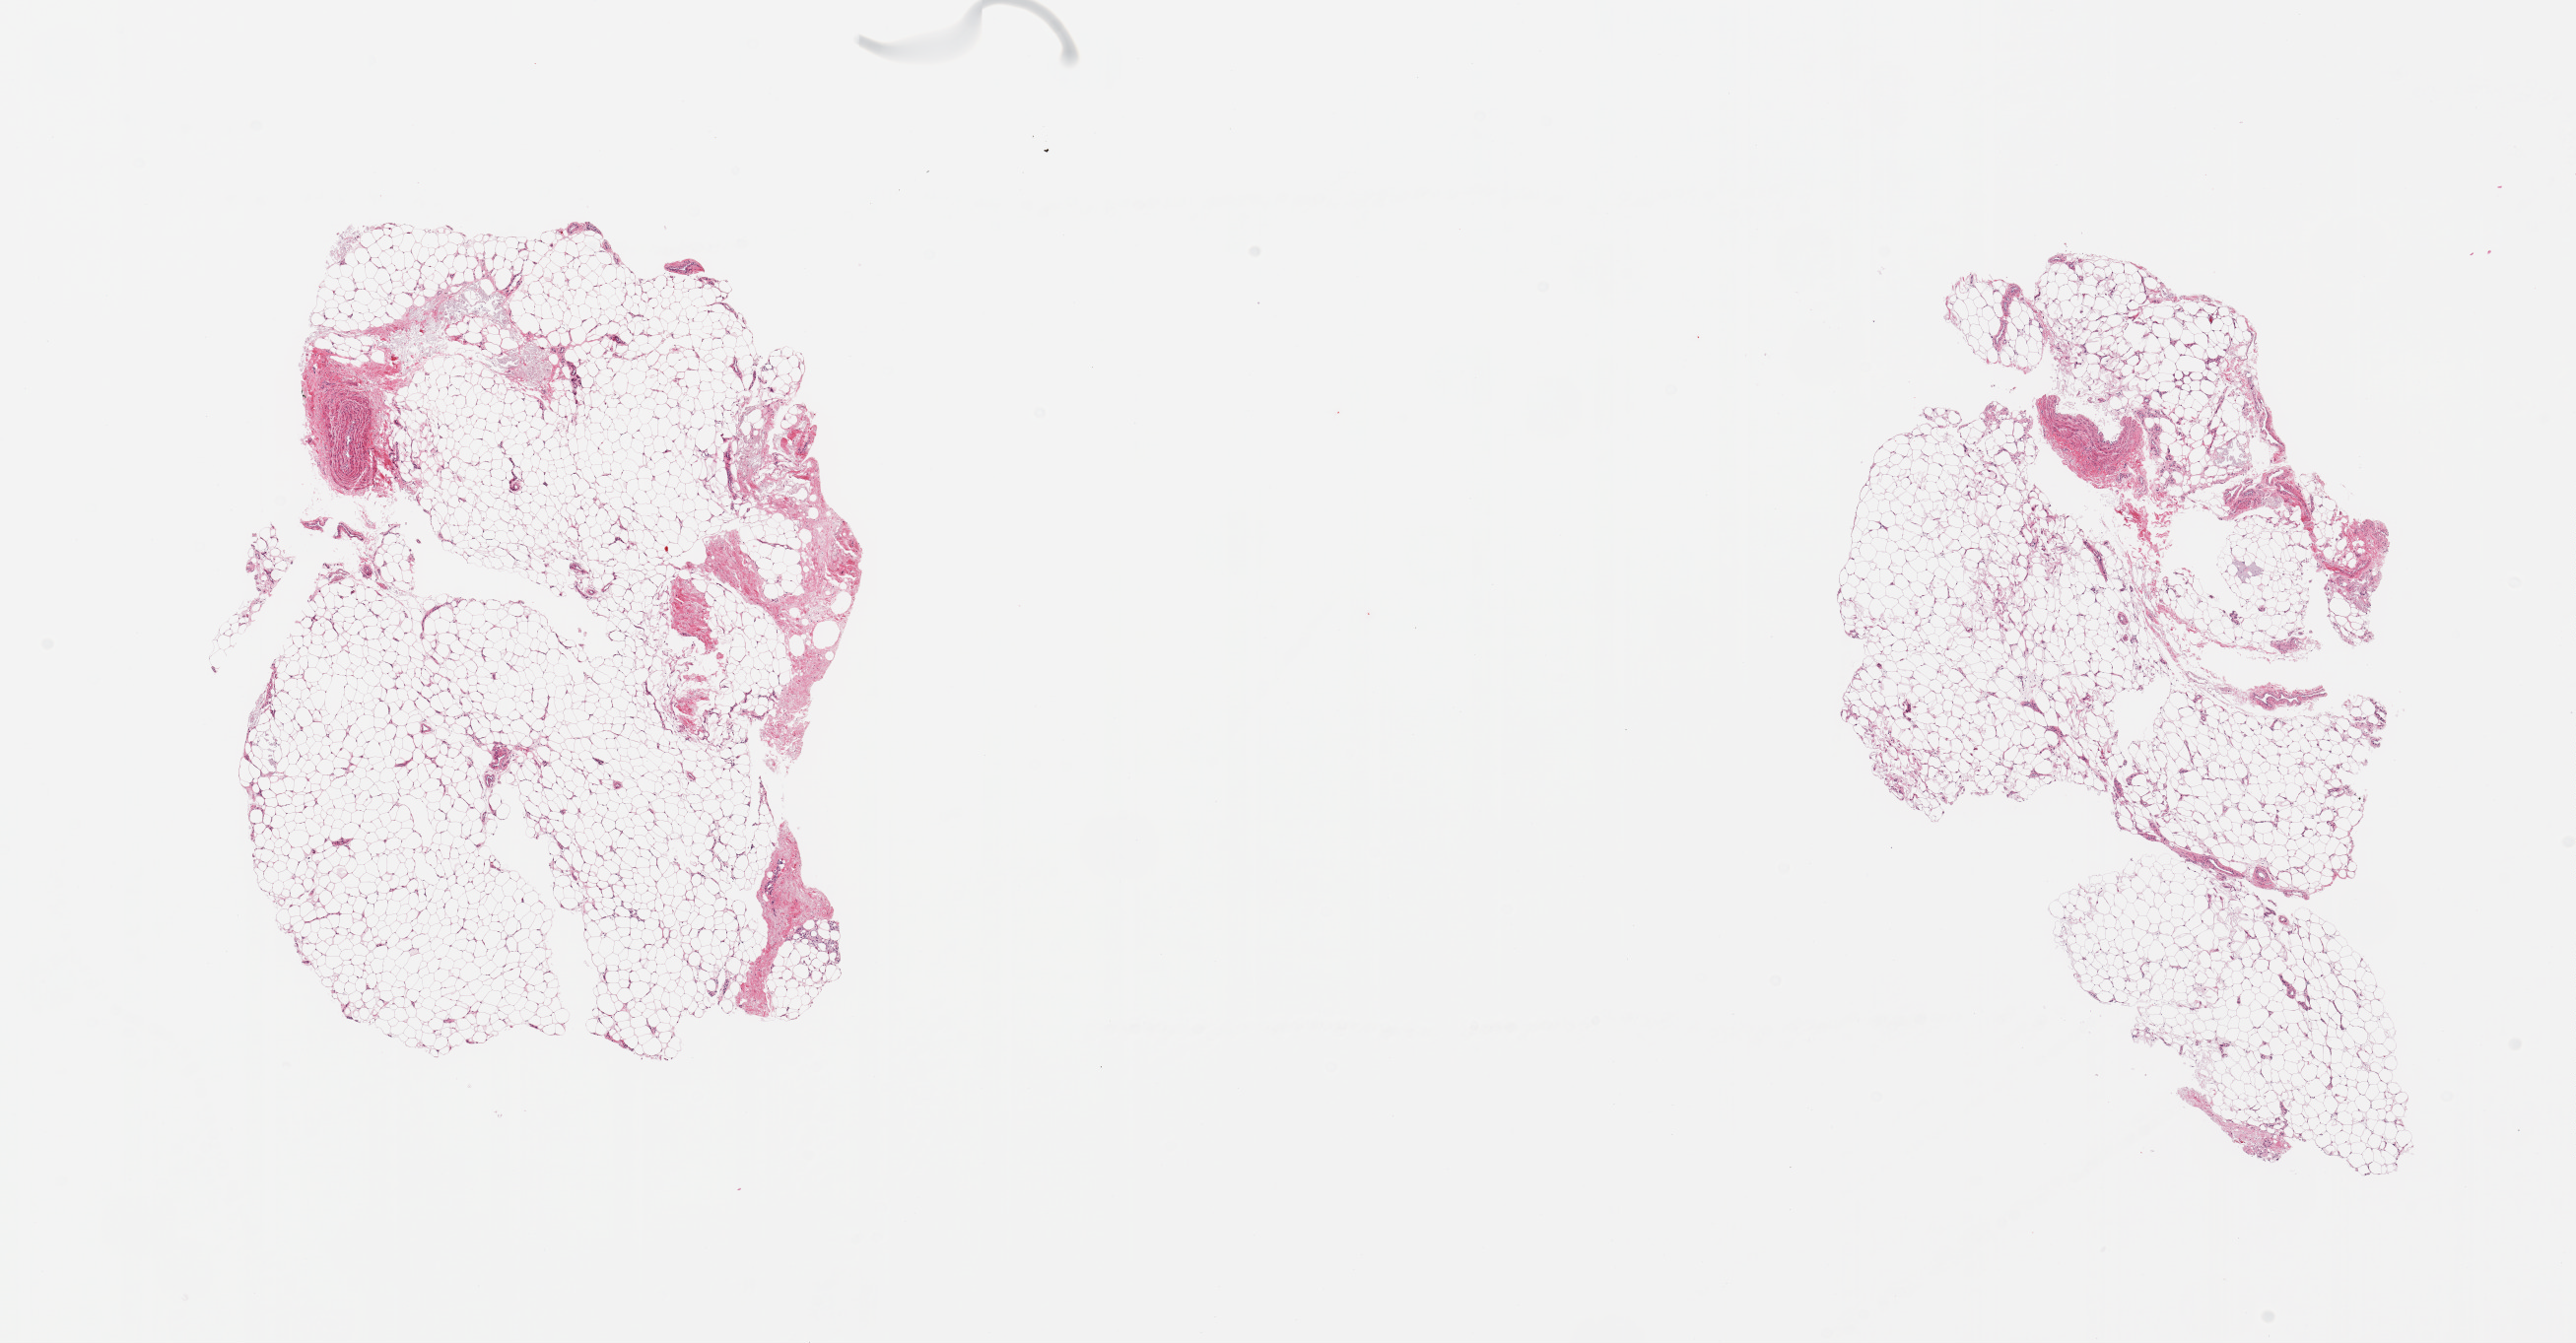
Hematoxylin and eosin (H&E) whole-slide image, low-resolution overview of the scanned area, about 20.7 x 10.8 mm (acquisition: 20x scan). PAXgene-fixed paraffin-embedded (PFPE) section. Sampled site (target tissue): adipose tissue. Tissue donor sample. Donor sex: female.
* reviewer comment on this tissue sample: 2 pieces; 5% fibrovascular content